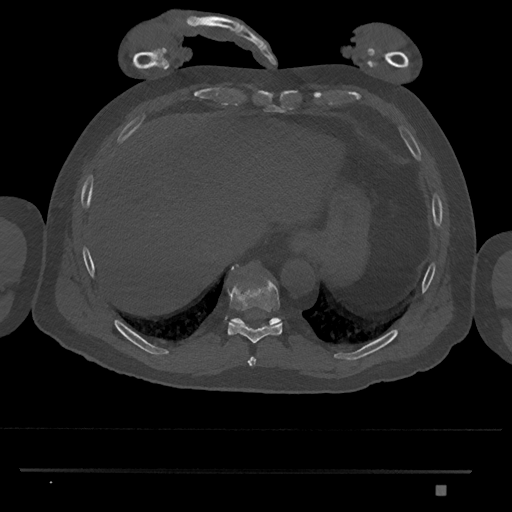
CT including the spine, one axial slice. Position 1044 of 1134 along the scan axis. Bone window (W 1800 / L 400 HU). 512 × 512 image matrix, field of view 429 × 429 mm. Male patient, age 65 years. From the clinical record (not read from this slice): primary cancer: prostate.
Annotated regions visible in this slice (semi-automatic segmentation, software-assisted and operator-edited):
- T10 vertebra: bounding box <231,318,282,325> (left, top, right, bottom; pixels)
- T8 vertebra: <248,356,256,366>
- T9 vertebra: <228,267,282,344>